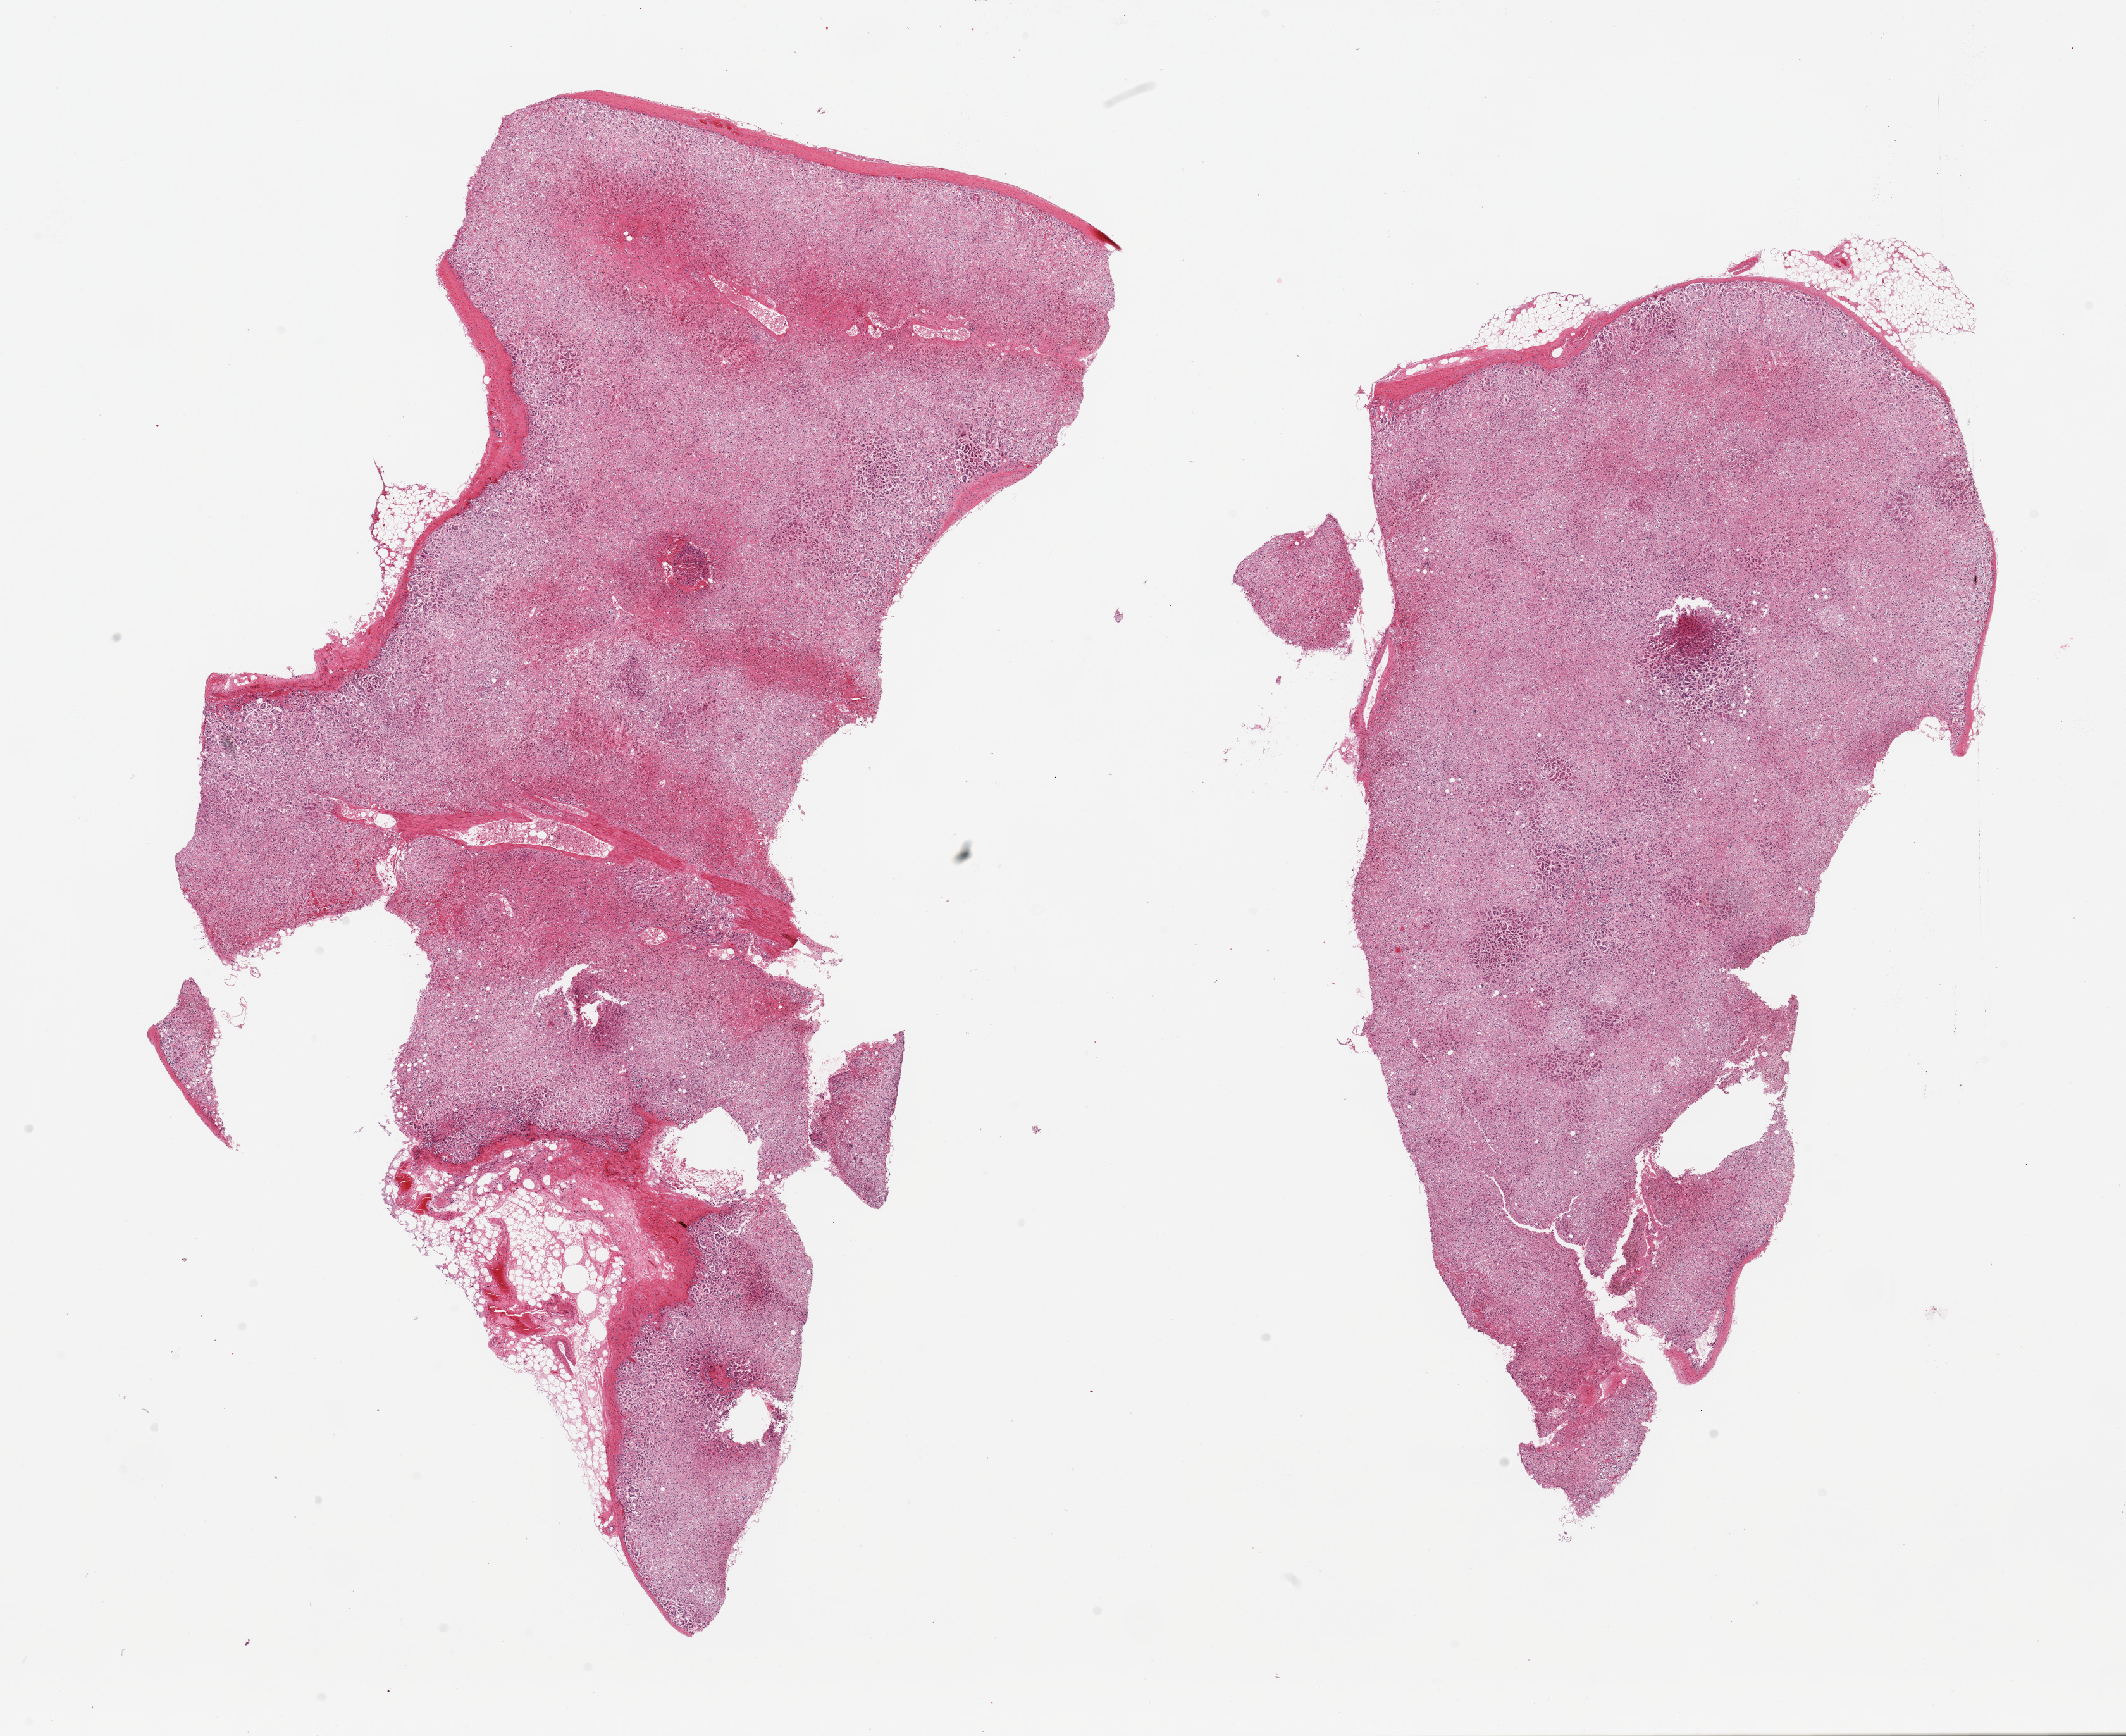
Haematoxylin and eosin whole-slide image — whole scanned area (about 26.6 x 21.7 mm) shown as a low-resolution overview; PAXgene-fixed, paraffin-embedded tissue; target tissue: adrenal gland; donor tissue sample. Male donor.
Pathologist's review note for this sample: 2 pieces; mostly cortex.